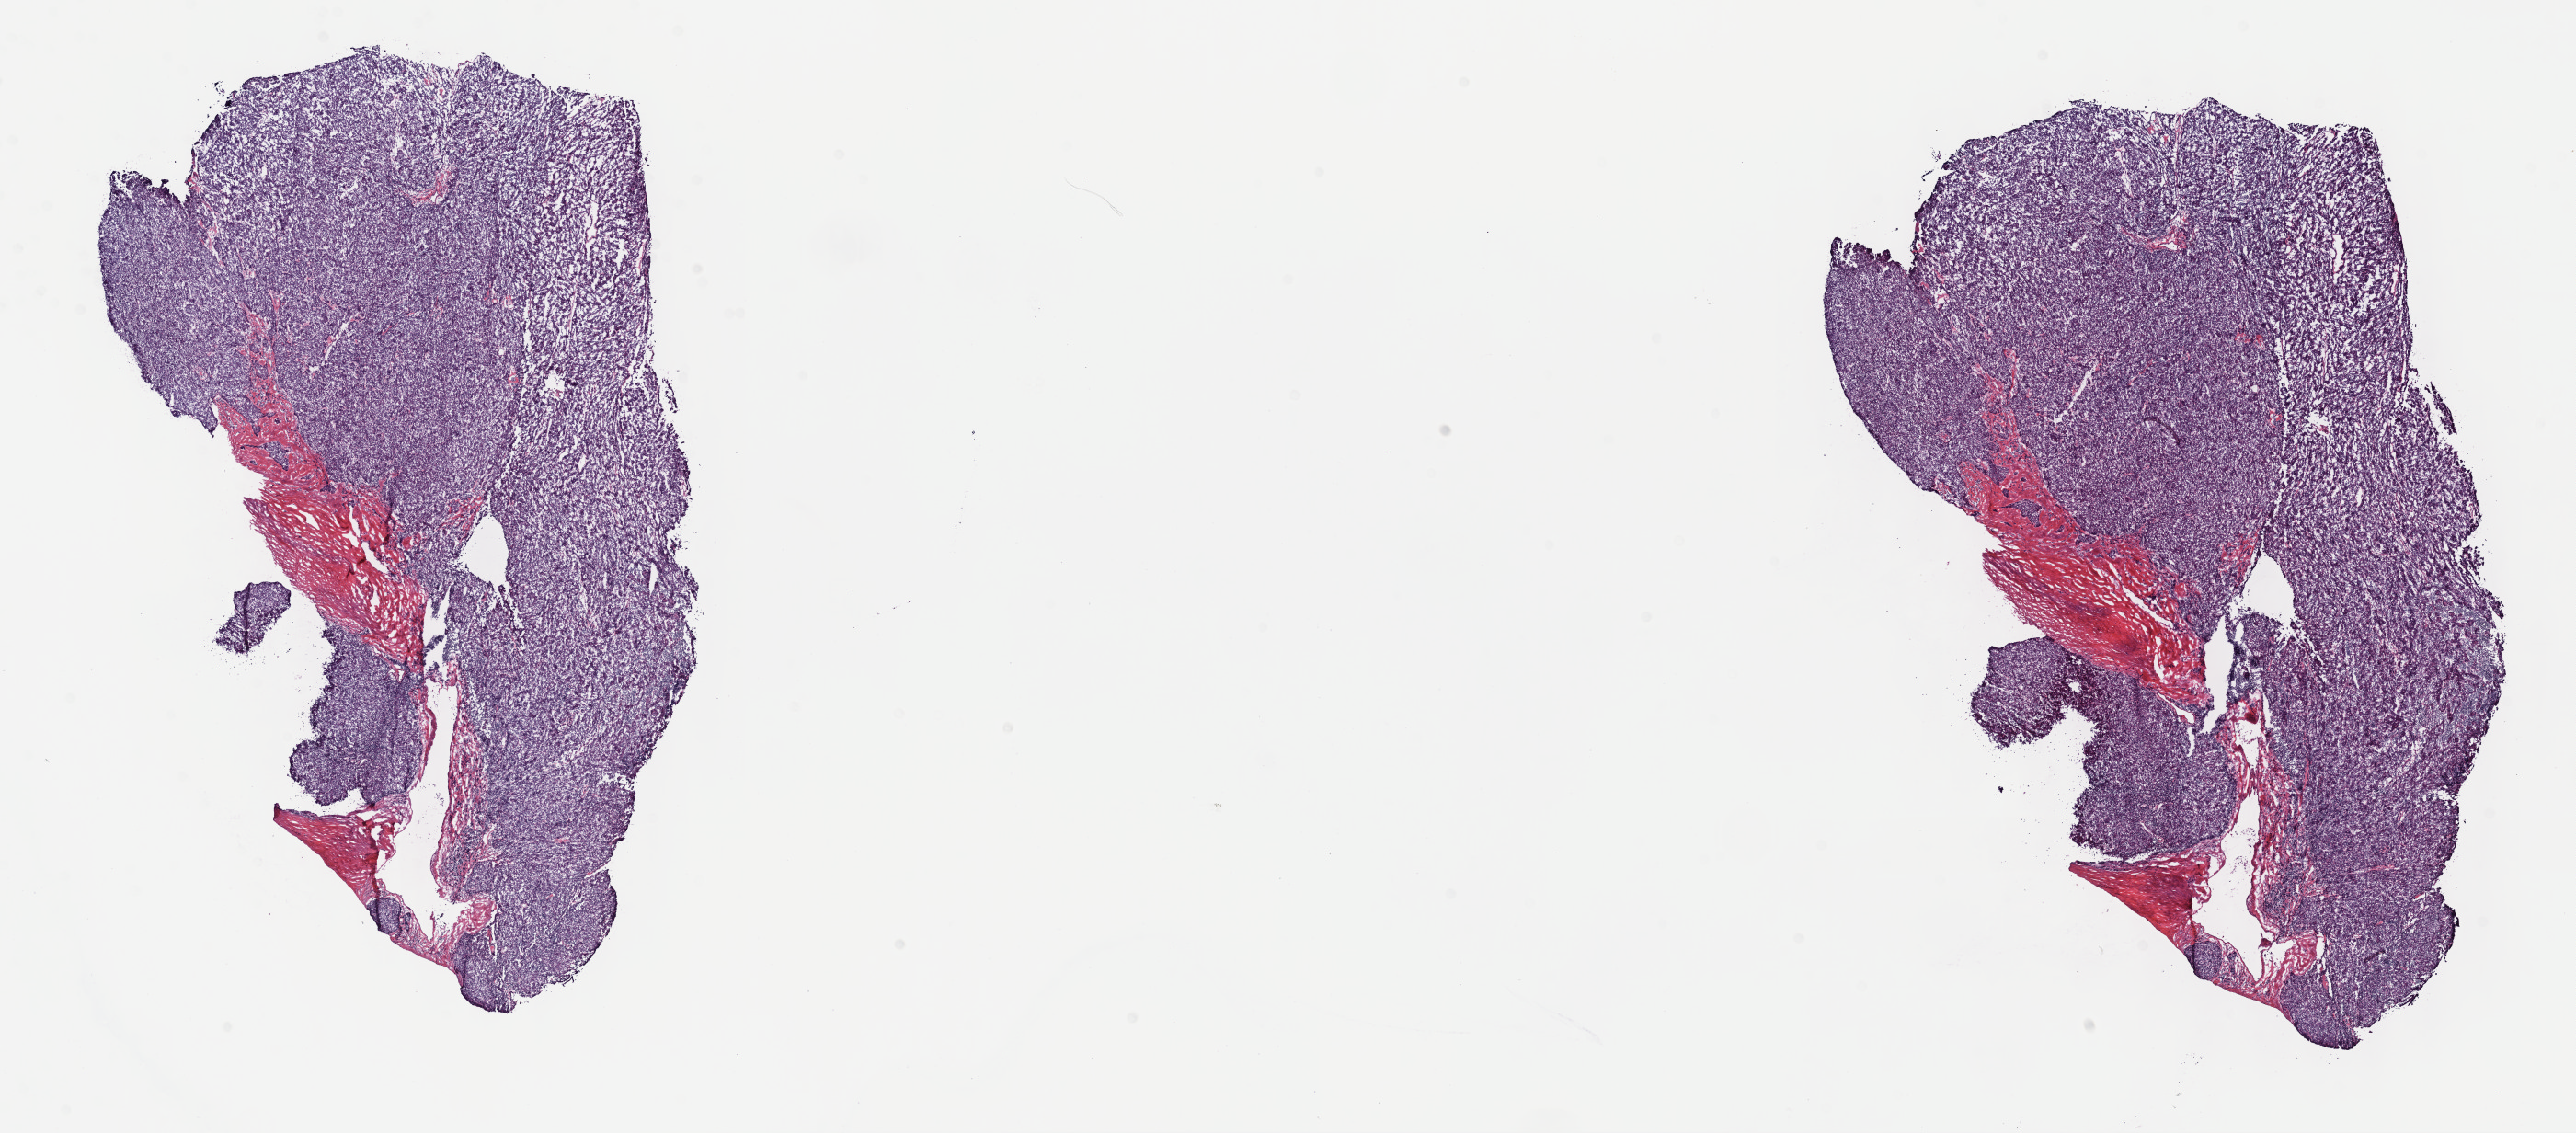
Digitized Hematoxylin and eosin (H&E) stained tissue section (whole slide) — shown as a low-resolution overview of the whole scanned area (about 22.7 x 10.0 mm); frozen section from the top of the tissue portion; primary tumour sample from the thymus. Male, age 60 years at initial diagnosis. Composition of this section per pathologist review: tumour cells 90%, tumour nuclei 98%, normal cells 0%, stromal cells 10%, necrosis 0%. Infiltration values recorded for this section: lymphocyte infiltration 0%, monocyte infiltration 0%, neutrophil infiltration 0%.
* diagnosis: Thymoma, type A, malignant